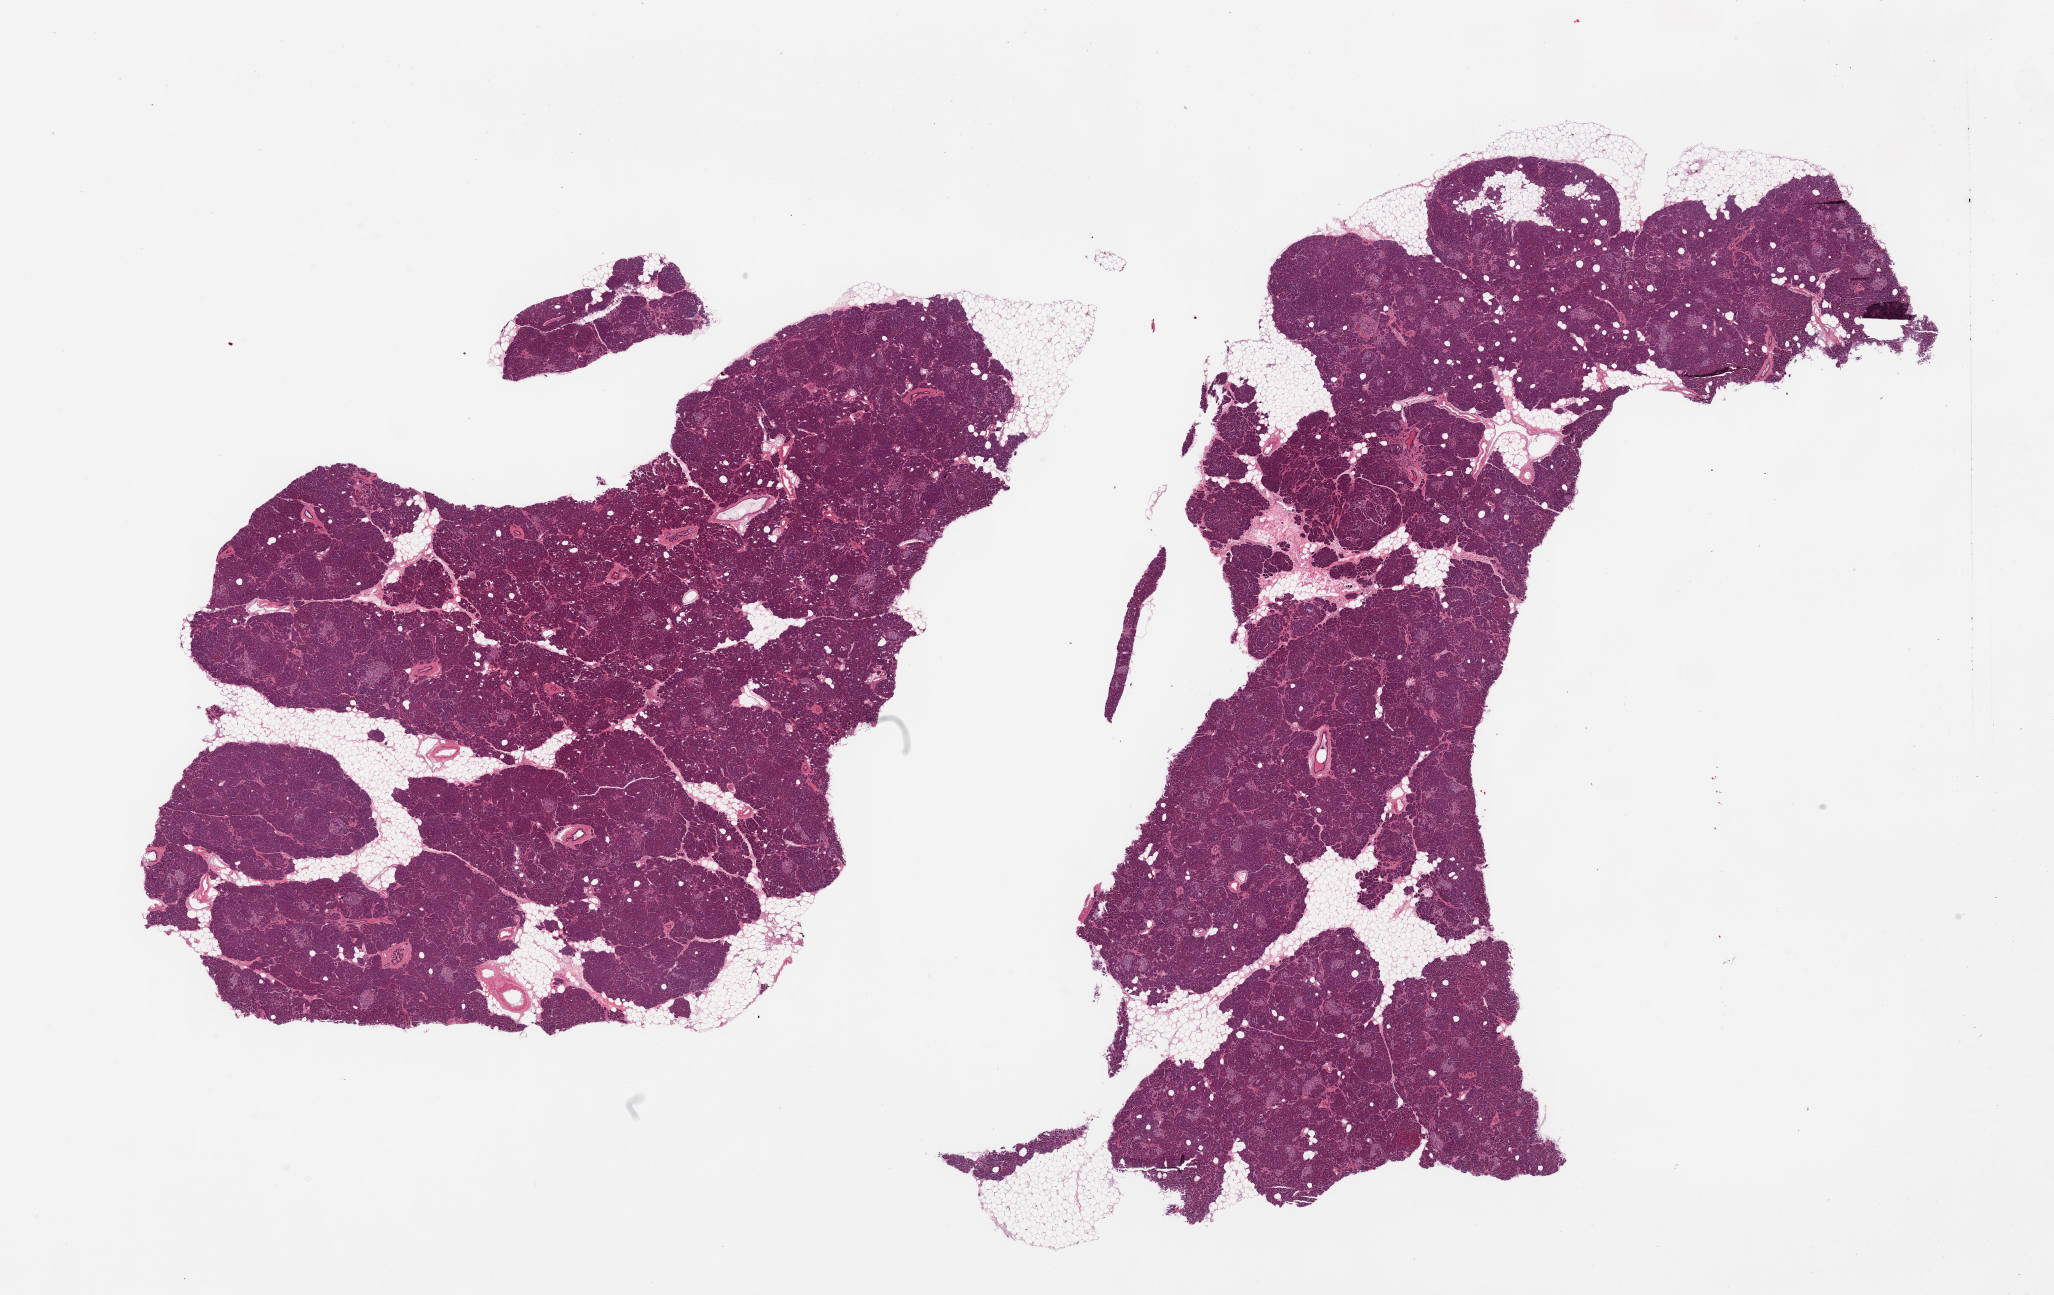
Haematoxylin and eosin whole-slide image, brightfield — low-resolution overview of the scanned area, about 32.5 x 20.5 mm. PAXgene-fixed, paraffin-embedded tissue. Sampled site (target tissue): pancreas. Donor tissue sample. Female donor.
• reviewer comment on this tissue sample: 2 pieces. 10% fat; numerous islets